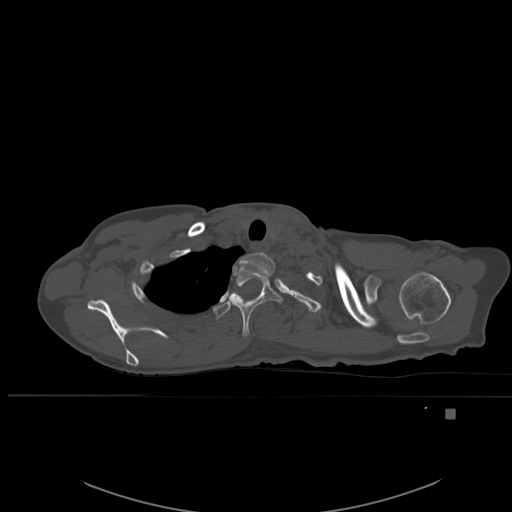
CT including the spine, one axial slice; position 435 of 537 along the scan axis; bone window (W 1800 / L 400 HU); 512 × 512 image matrix, field of view 440 × 440 mm. Female patient, age 45 years. Case-level facts recorded for this patient, not image findings: primary cancer: lung.
Structures marked on this image (semi-automatic segmentation, software-assisted and operator-edited):
- T1 vertebra: bounding box [x1, y1, x2, y2] px = [233, 252, 276, 276]
- T2 vertebra: [229, 264, 282, 337]
- T3 vertebra: [213, 292, 237, 319]